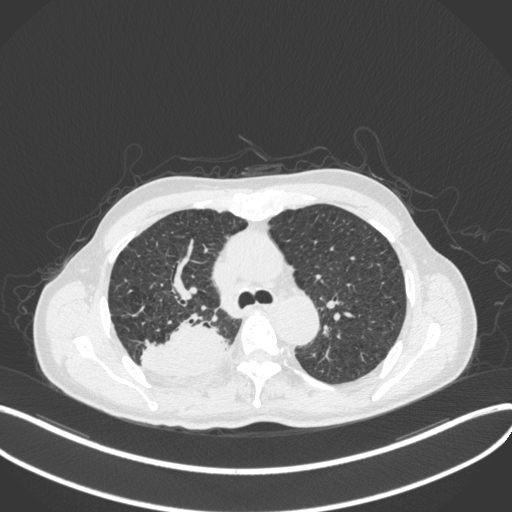
Chest CT, one axial slice; lung window (W 1500 / L -600 HU); 1 mm slice thickness; 512 × 512 image matrix, field of view 400 × 400 mm. Male patient, age 79 years. Case-level facts recorded for this patient, not image findings: clinical TNM (as recorded): T3 N0 M0.
Structures marked on this image (bounding box drawn by a radiologist):
- lung tumour (recorded histology: adenocarcinoma): bounding box [x1, y1, x2, y2] px = [138, 310, 233, 380]